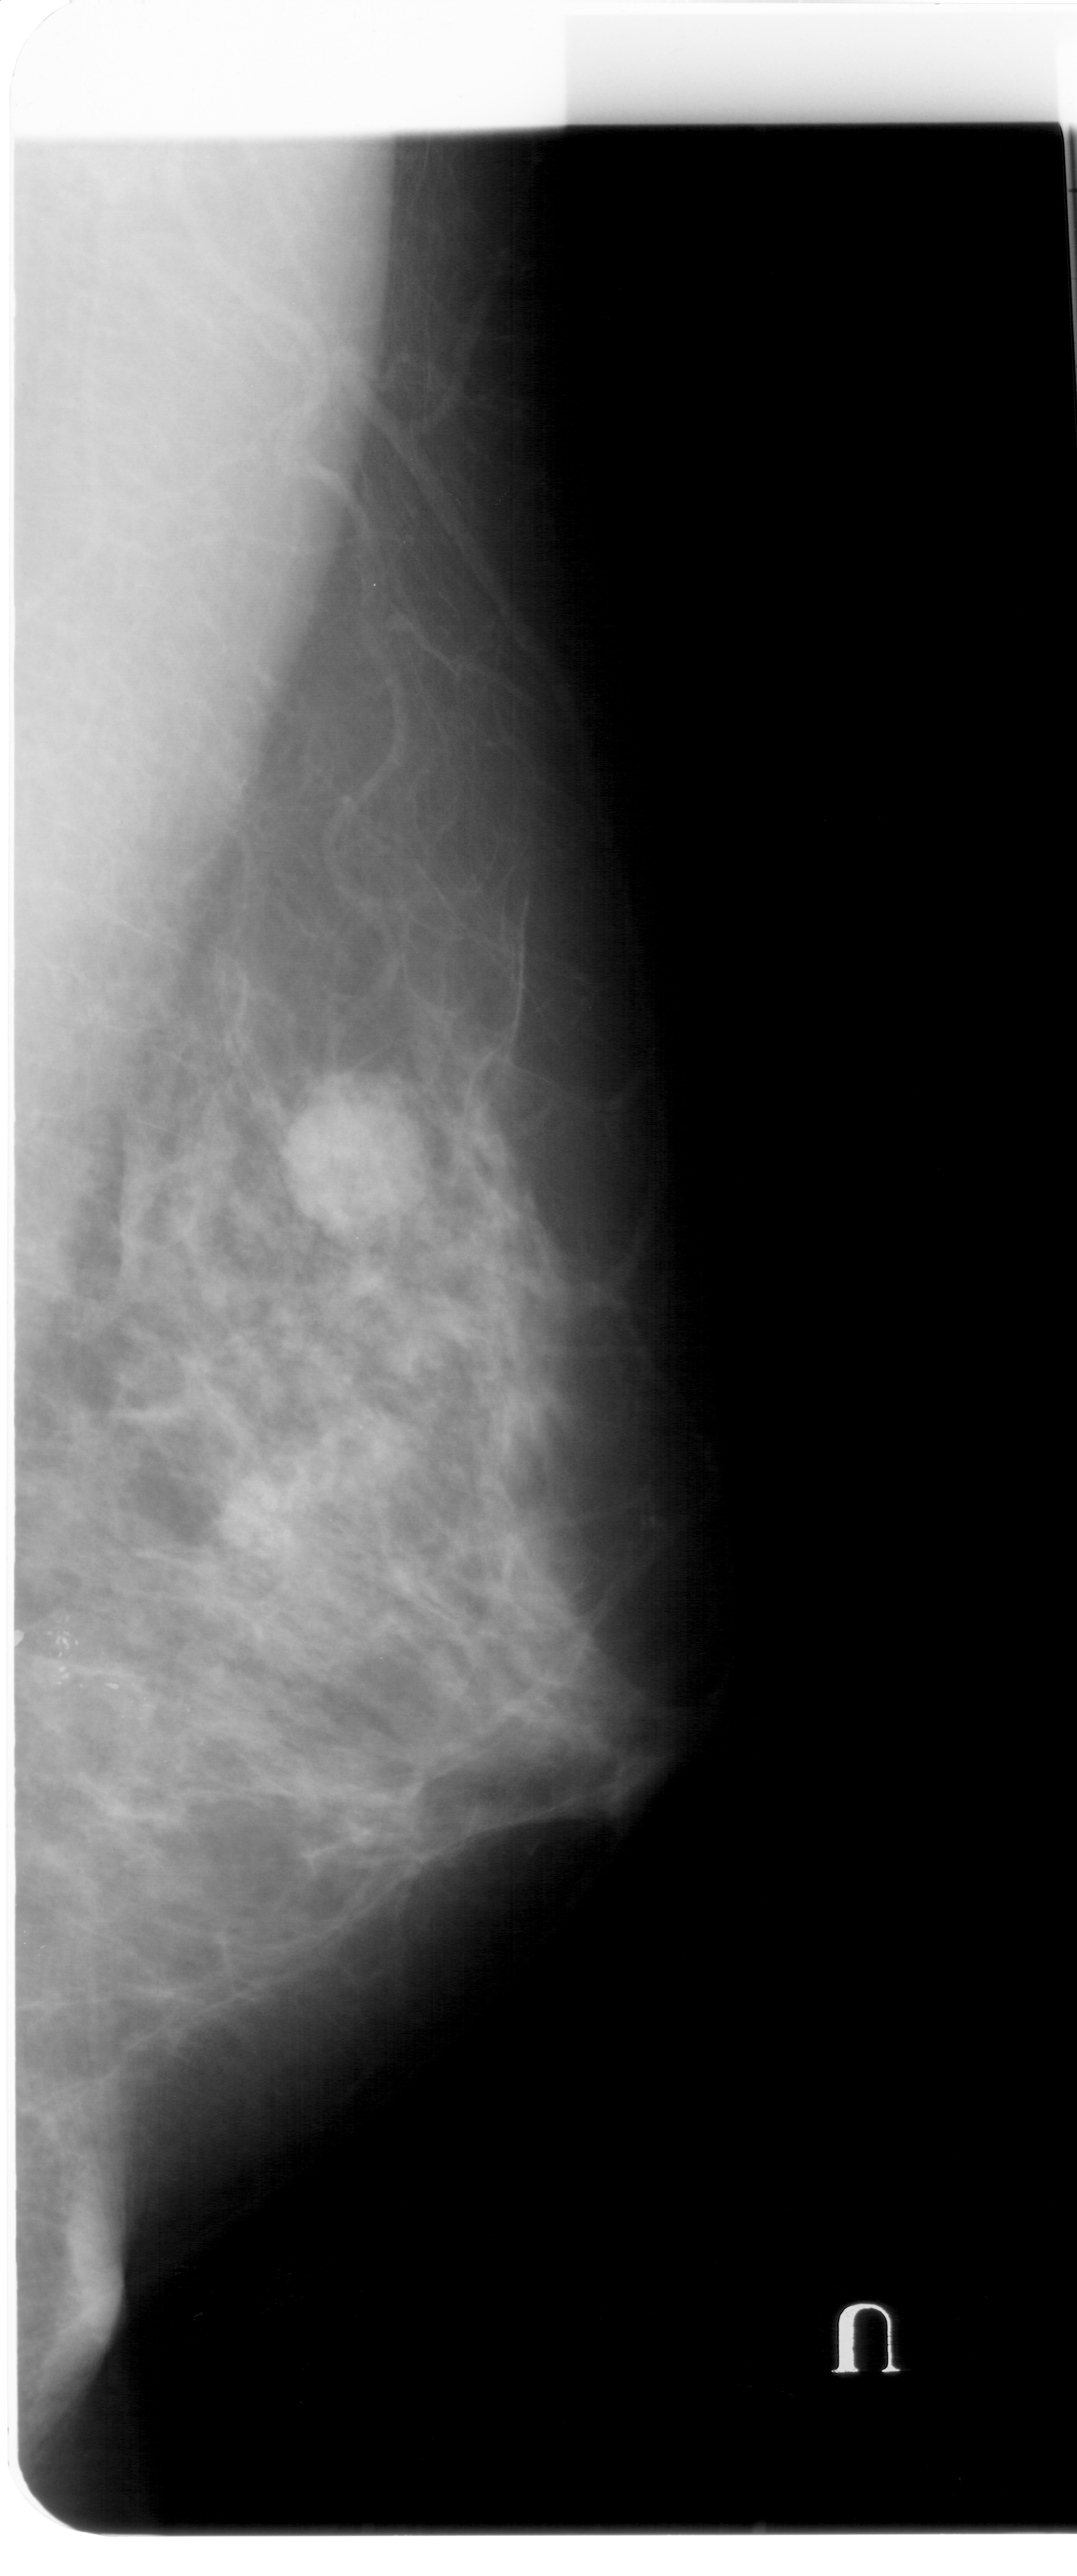
Digitized screen-film mammogram, right breast, mediolateral oblique (MLO) view, breast composition: heterogeneously dense (BI-RADS density category 3 of 4).
Abnormality record for this image: calcifications, morphology pleomorphic, distribution clustered; BI-RADS assessment category 4; subtlety rating 3 on a 1 (subtle) to 5 (obvious) scale; pathology result (as recorded, not read from the image): malignant.